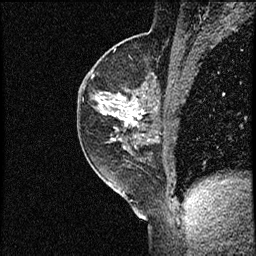
Breast MRI (dynamic contrast-enhanced), one sagittal slice; dynamic contrast-enhanced study with each time point stored as its own series, time point 2 of 3 at this slice position (early post-contrast, ordered by acquisition time); 1.5 T; TE 4.2 ms, TR 17.3 ms; 2 mm slice thickness; 256 × 256 image matrix, field of view 200 × 200 mm. Female patient. From the clinical record (not read from this slice): setting: breast cancer imaged before/during neoadjuvant chemotherapy; receptor status: HER2-positive.
Annotated regions visible in this slice (semi-automatically segmented with operator editing):
- analysis volume of interest (the breast-tissue region the enhancement analysis was run in; not a lesion): bounding box (x1, y1, x2, y2) in pixels: (77, 50, 156, 155)
- tumour enhancement mask (voxels above the 100 % enhancement threshold inside the analysis volume of interest): (100, 93, 146, 126)